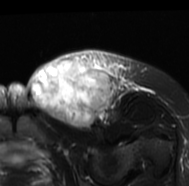
MRI of an extremity soft-tissue mass, one axial slice; slice 45 of 77 in the series (ordered by position); T2-weighted fat-saturated; MR volume resampled by the dataset authors to the PET/CT grid (not the native acquisition matrix); 3.27 mm slice thickness; 189 × 186 image matrix. Female patient. Case-level facts recorded for this patient, not image findings: histological type: leiomyosarcoma; grade: high; site of the primary tumour: groin.
Outlined on this slice (expert contour drawn on MRI and transferred to this co-registered scan by the dataset authors):
- gross tumour volume including surrounding oedema: box from (x=28, y=49) to (x=148, y=130) px
- gross tumour volume (mass): (x=29, y=56)–(x=114, y=130)